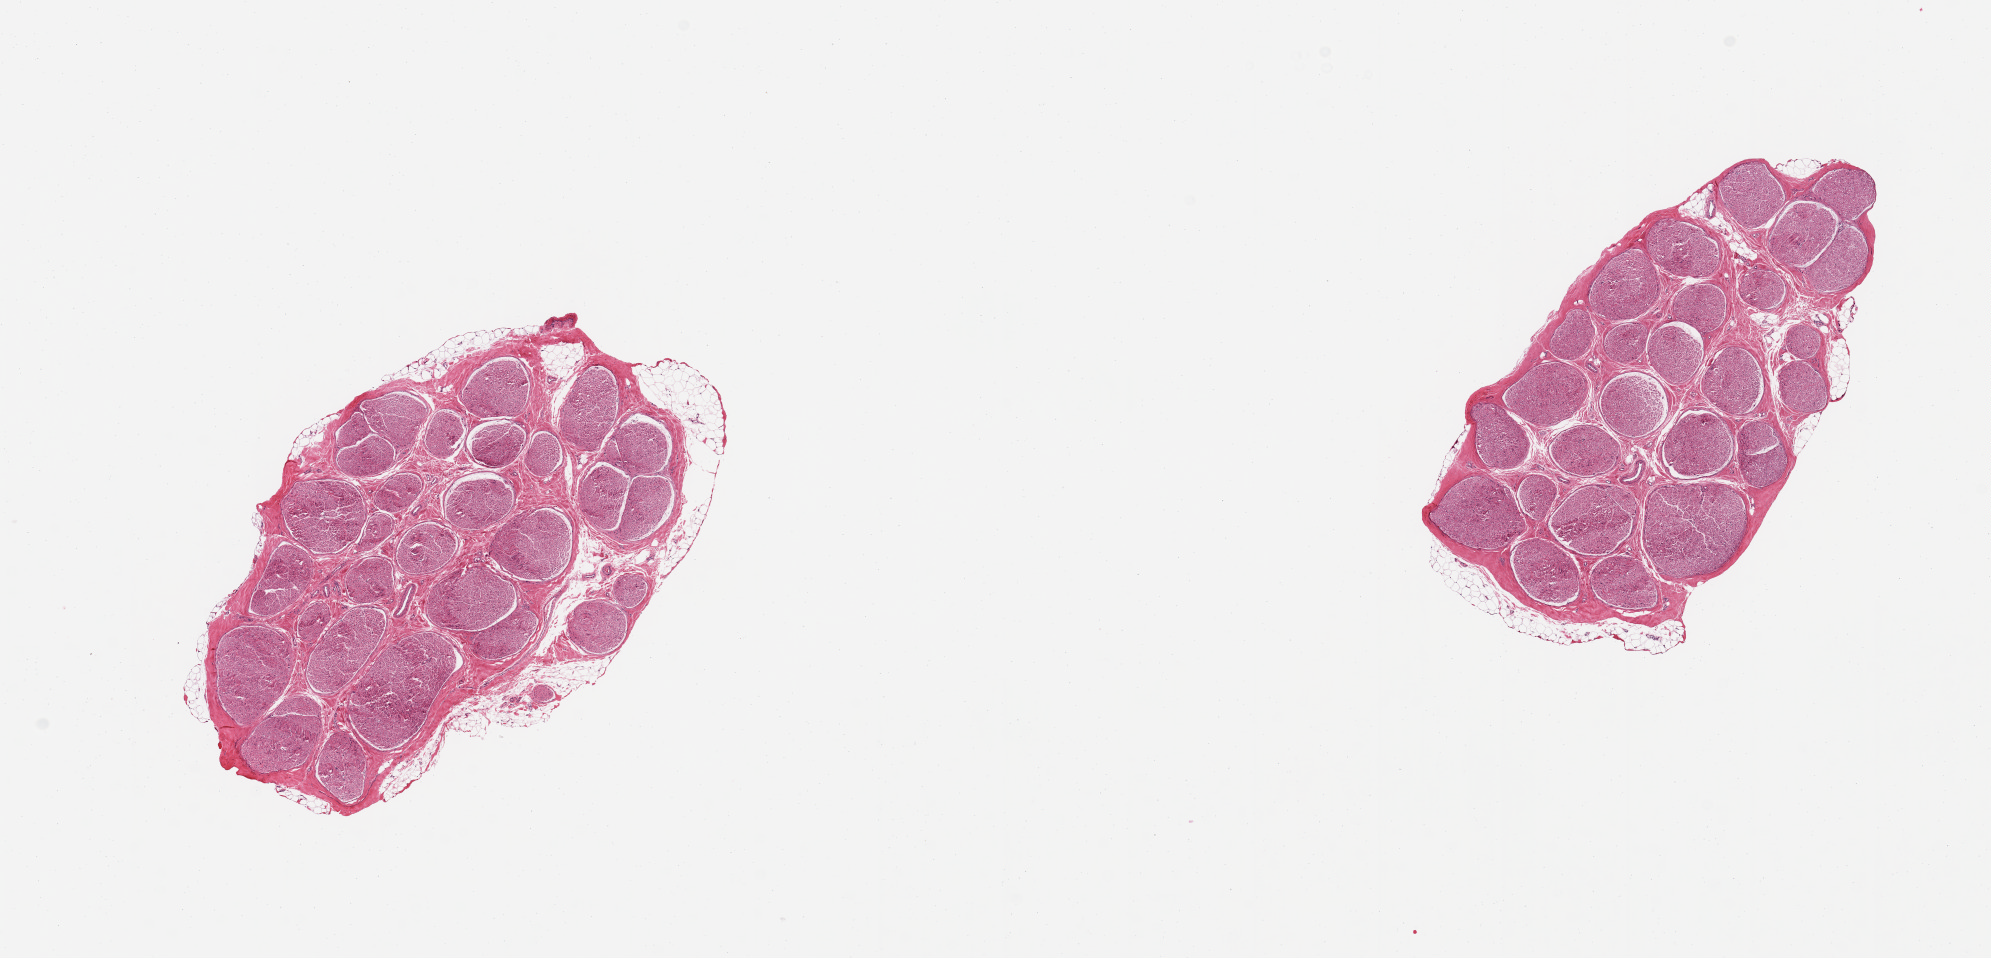
Whole-slide image, H&E stain, a low-resolution overview of the entire scanned area, about 15.8 x 7.6 mm; PAXgene-fixed paraffin-embedded (PFPE) section; section of tibial nerve (target tissue); tissue donor sample. Female donor.
Pathologist's review note for this sample: 2 pieces; <10% attached fat.